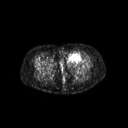
FDG PET of an extremity soft-tissue mass (from a PET/CT study), one axial slice. Position 38 of 267 along the scan axis. 3.27 mm slice thickness. 128 × 128 image matrix, field of view 700 × 700 mm. Female patient, age 47 years. Case-level facts recorded for this patient, not image findings: histological type: myxofibrosarcoma; grade: intermediate; site of the primary tumour: left thigh.
Outlined on this slice (expert contour drawn on MRI and transferred to this co-registered scan by the dataset authors):
- gross tumour volume including surrounding oedema: bounding box <65,52,83,64> (left, top, right, bottom; pixels)
- gross tumour volume (mass): <67,52,81,62>